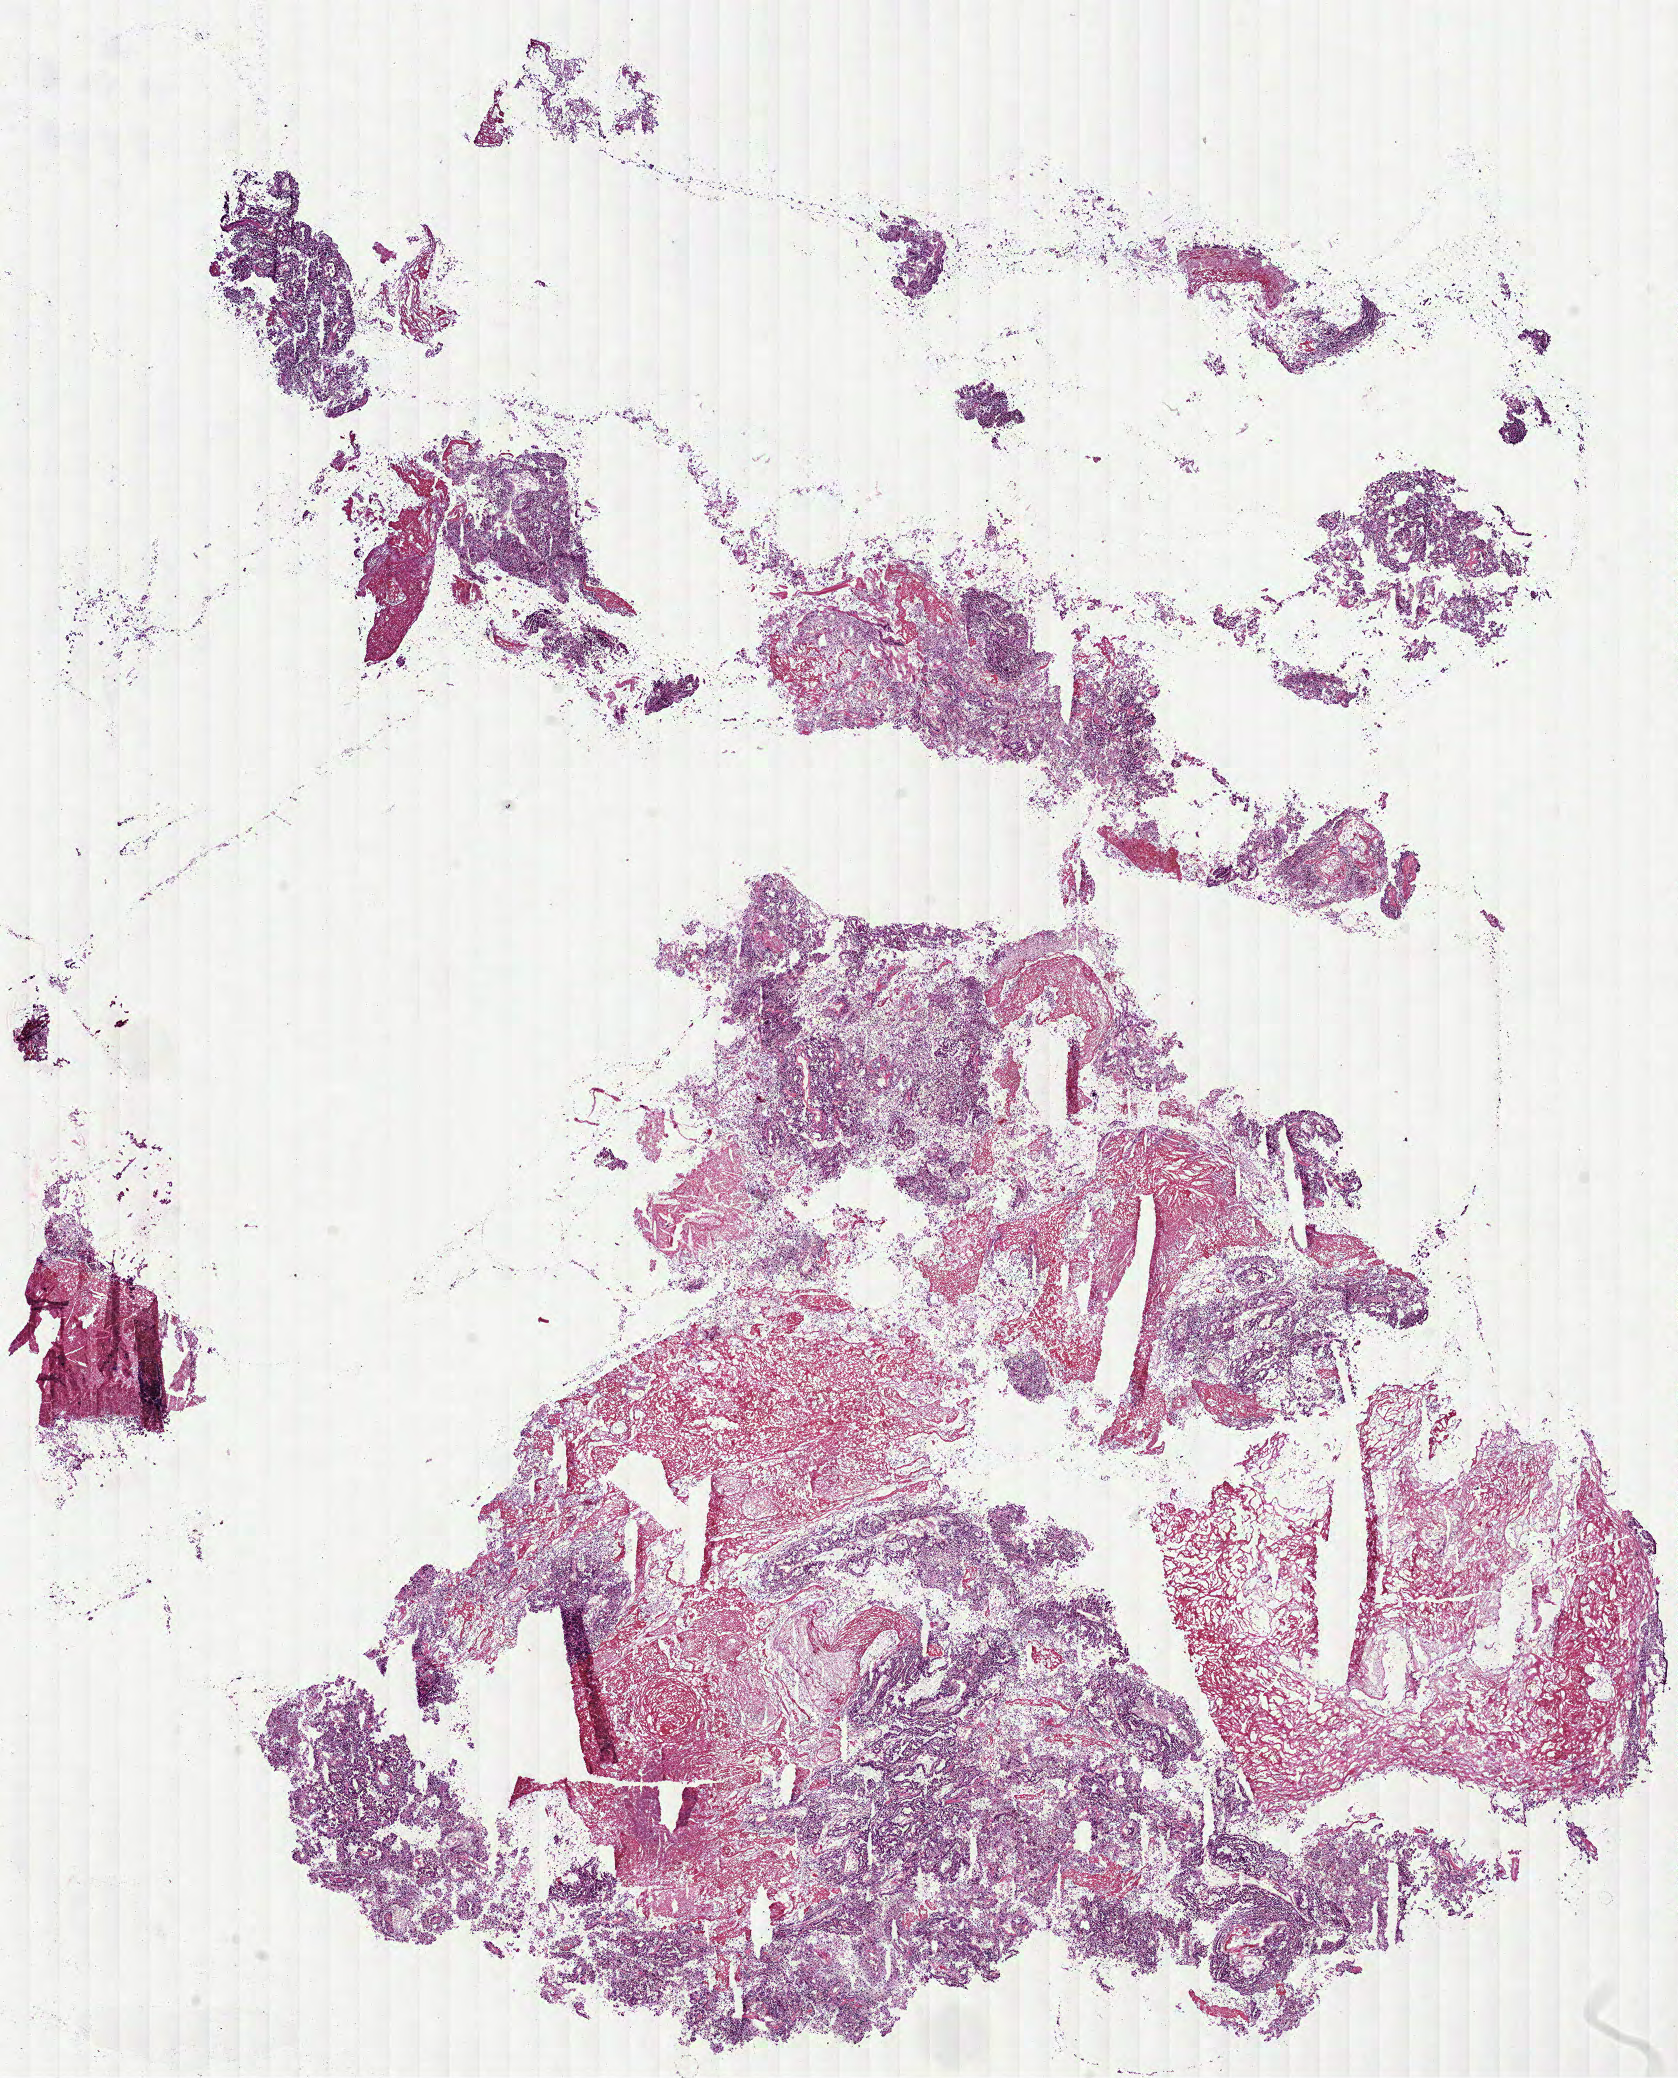
Digitized Hematoxylin and eosin (H&E) stained tissue section (whole slide) — whole scanned area (about 13.5 x 16.8 mm, acquisition: 40x scan) shown as a low-resolution overview, frozen section from the bottom of the tissue portion, primary tumour sample from the kidney. Male patient; age at initial diagnosis 69 years. Pathologist review of this section (percent, as recorded): tumour cells 55%, tumour nuclei 75%, normal cells 0%, stromal cells 40%, necrosis 5%.
AJCC pathologic stage: III. Lymph nodes positive (case pathology): 0 of 9 examined. Pathologic diagnosis: Papillary adenocarcinoma, NOS.